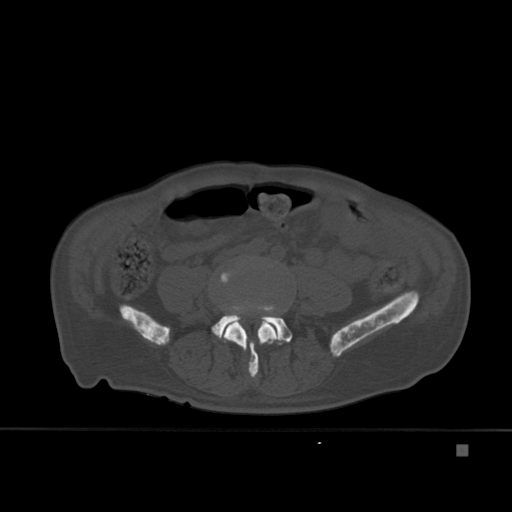
CT including the spine, one axial slice; slice 114 of 451 in the series (ordered by position); bone window (W 1800 / L 400 HU); 1.5 mm slice thickness; 512 × 512 image matrix, field of view 378 × 378 mm. Patient: male, 75 years. From the clinical record (not read from this slice): primary cancer: prostate.
Outlined on this slice (semi-automatic segmentation, software-assisted and operator-edited):
- L4 vertebra: bounding box <221,273,278,378> (left, top, right, bottom; pixels)
- L5 vertebra: <212,301,292,345>
- T7 vertebra: <211,308,284,329>